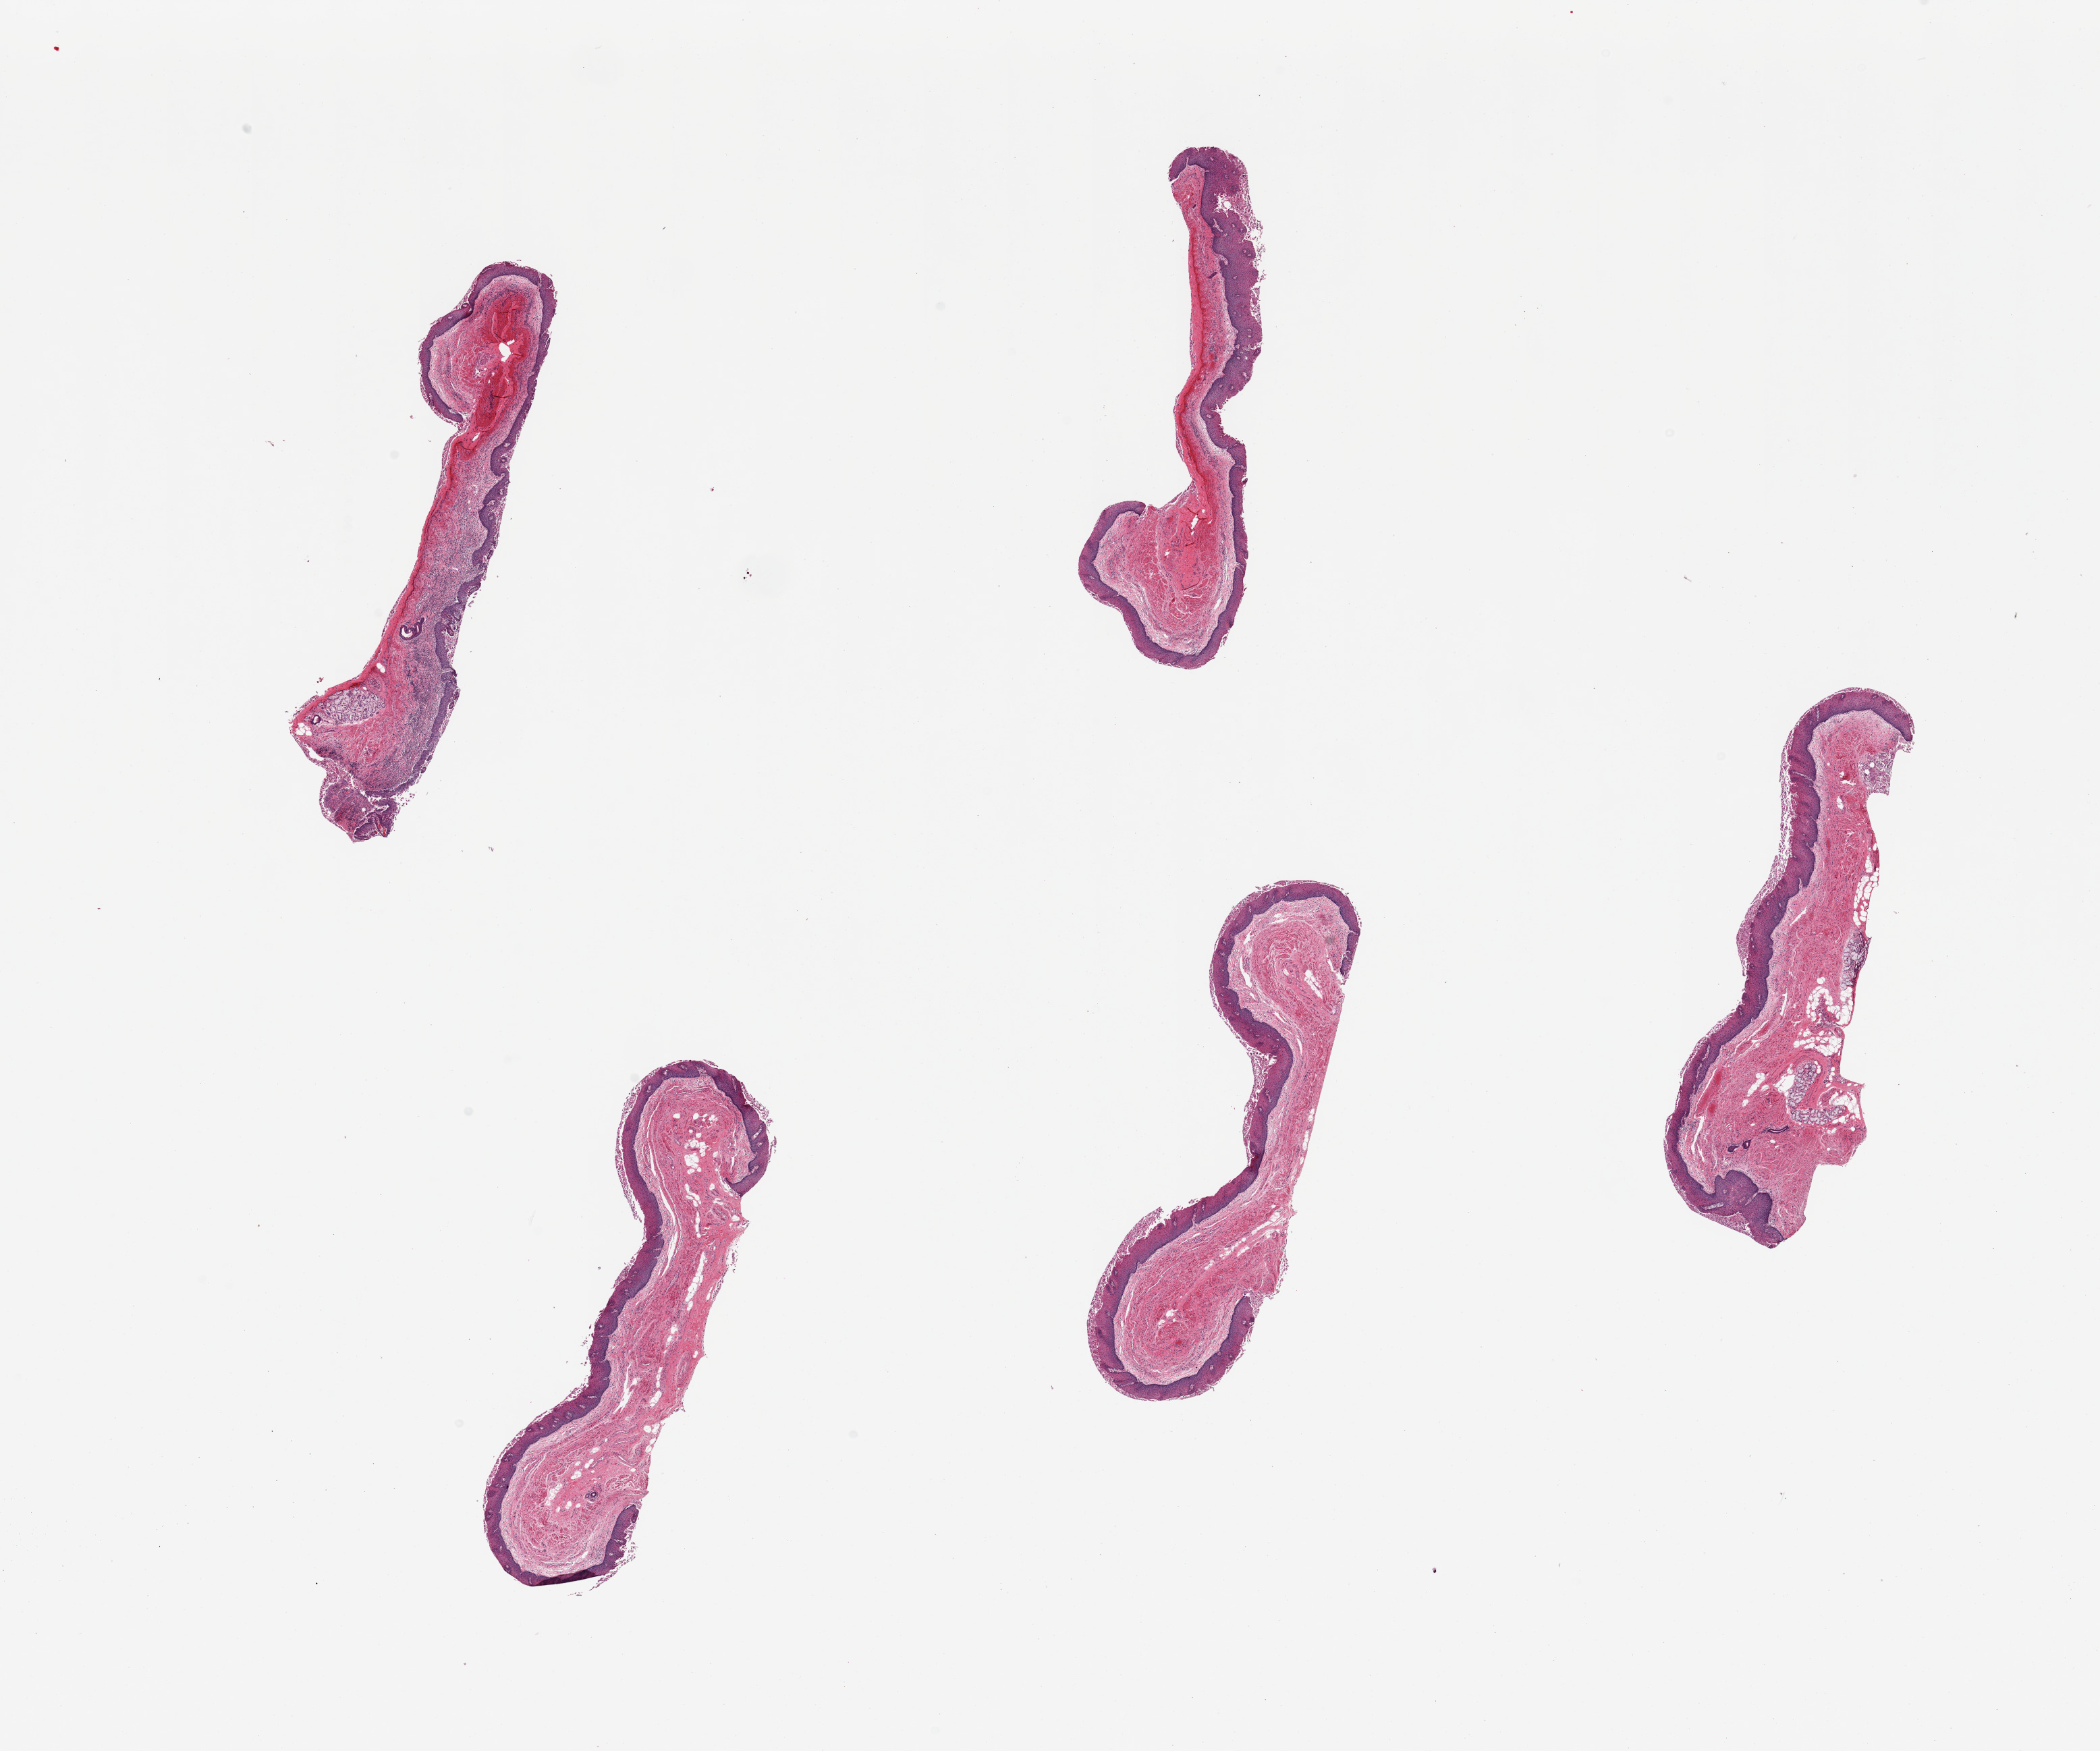
Digitized hematoxylin and eosin (H&E)-stained section, whole scanned area (about 24.6 x 20.5 mm) shown as a low-resolution overview. PAXgene-fixed paraffin-embedded (PFPE) section. Section of transverse colon (target tissue). Tissue donor sample. Female donor.
* pathologist's review note for this sample: 5 pieces, not colon, chronically inflamed squamous mucosa